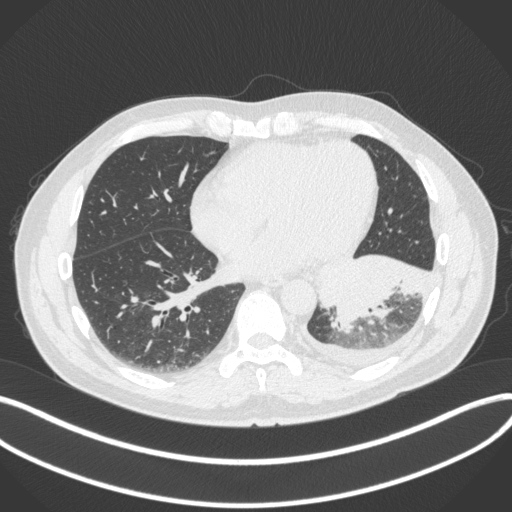
Chest CT, one axial slice; position 129 of 350 along the scan axis; reconstruction kernel B31f; 120 kVp; lung window (W 1500 / L -600 HU); 512 × 512 image matrix, field of view 400 × 400 mm. Patient: male, 58 years. Case-level facts recorded for this patient, not image findings: clinical TNM (as recorded): T3 N1 M1b.
Annotated regions visible in this slice (bounding box drawn by a radiologist):
- lung tumour (recorded histology: small cell carcinoma): bounding box (x1, y1, x2, y2) in pixels: (316, 250, 434, 331)